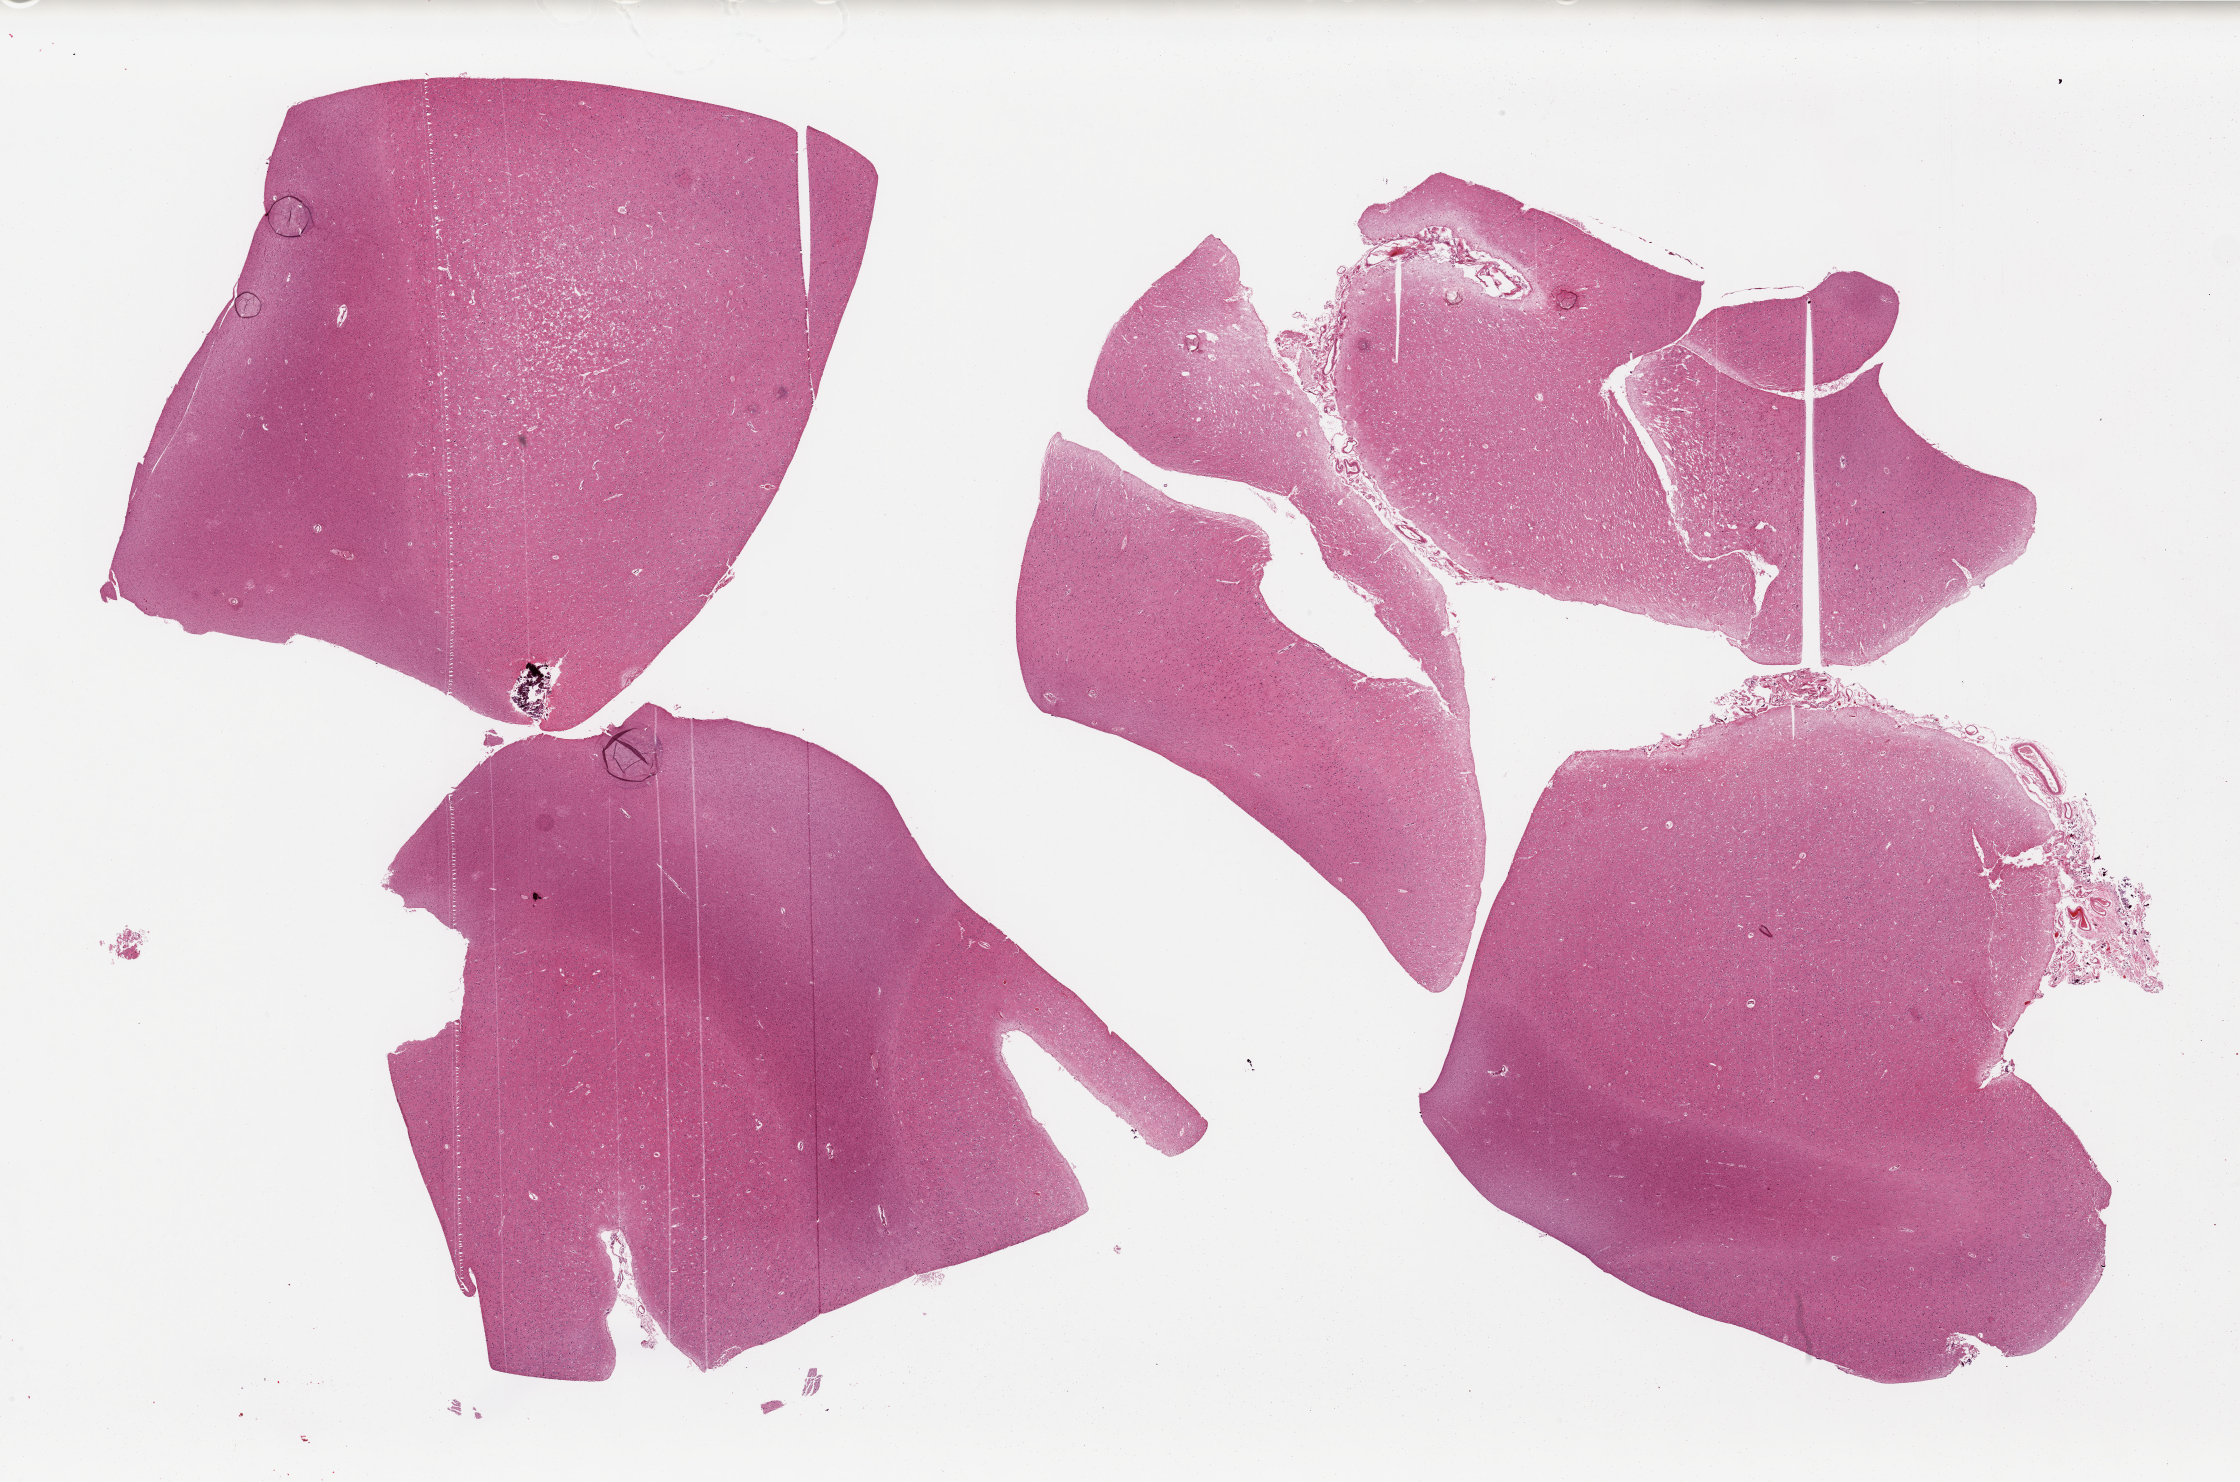
H&E whole-slide image, brightfield, whole scanned area (about 35.4 x 23.4 mm) shown as a low-resolution overview. PAXgene-fixed, paraffin-embedded tissue. Target tissue: cerebral cortex. Tissue donor sample. Donor: male.
• reviewer comment on this tissue sample: 4 pieces, no abnormalities